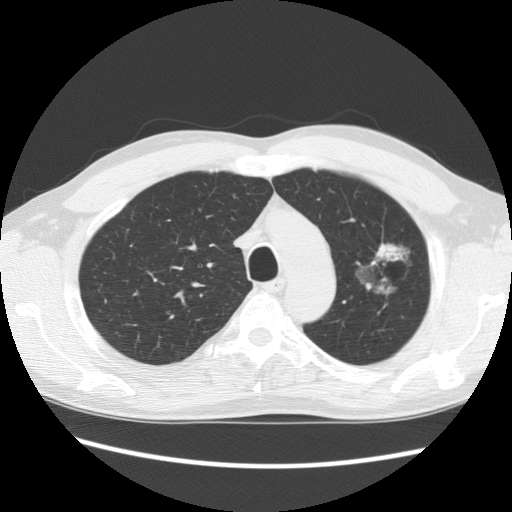
Axial slice from a low-dose chest CT screening exam; second annual screen; lung window (W 1500 / L -600 HU); 2.5 mm slice thickness; standard (soft-tissue) reconstruction kernel (STANDARD). Male, age 61 years at enrolment.
• Lesion marked by an expert reader, box from (x=344, y=224) to (x=425, y=301) px.
• Reader record for this screening exam (exam-level; its link to the box is not recorded): non-calcified nodule or mass ≥4 mm, left upper lobe, 34 × 32 mm, poorly defined margins, mixed attenuation, pre-existing on the prior screen: yes; interval growth: no.
• Official screen result: positive, no significant change: stable abnormalities potentially related to lung cancer, unchanged since the prior screening exam.
• Lung cancer was diagnosed 704 days after this screen: bronchiolo-alveolar adenocarcinoma, NOS, left upper lobe, well differentiated (G1), stage IB (AJCC 6th edition), 44 mm at pathology.